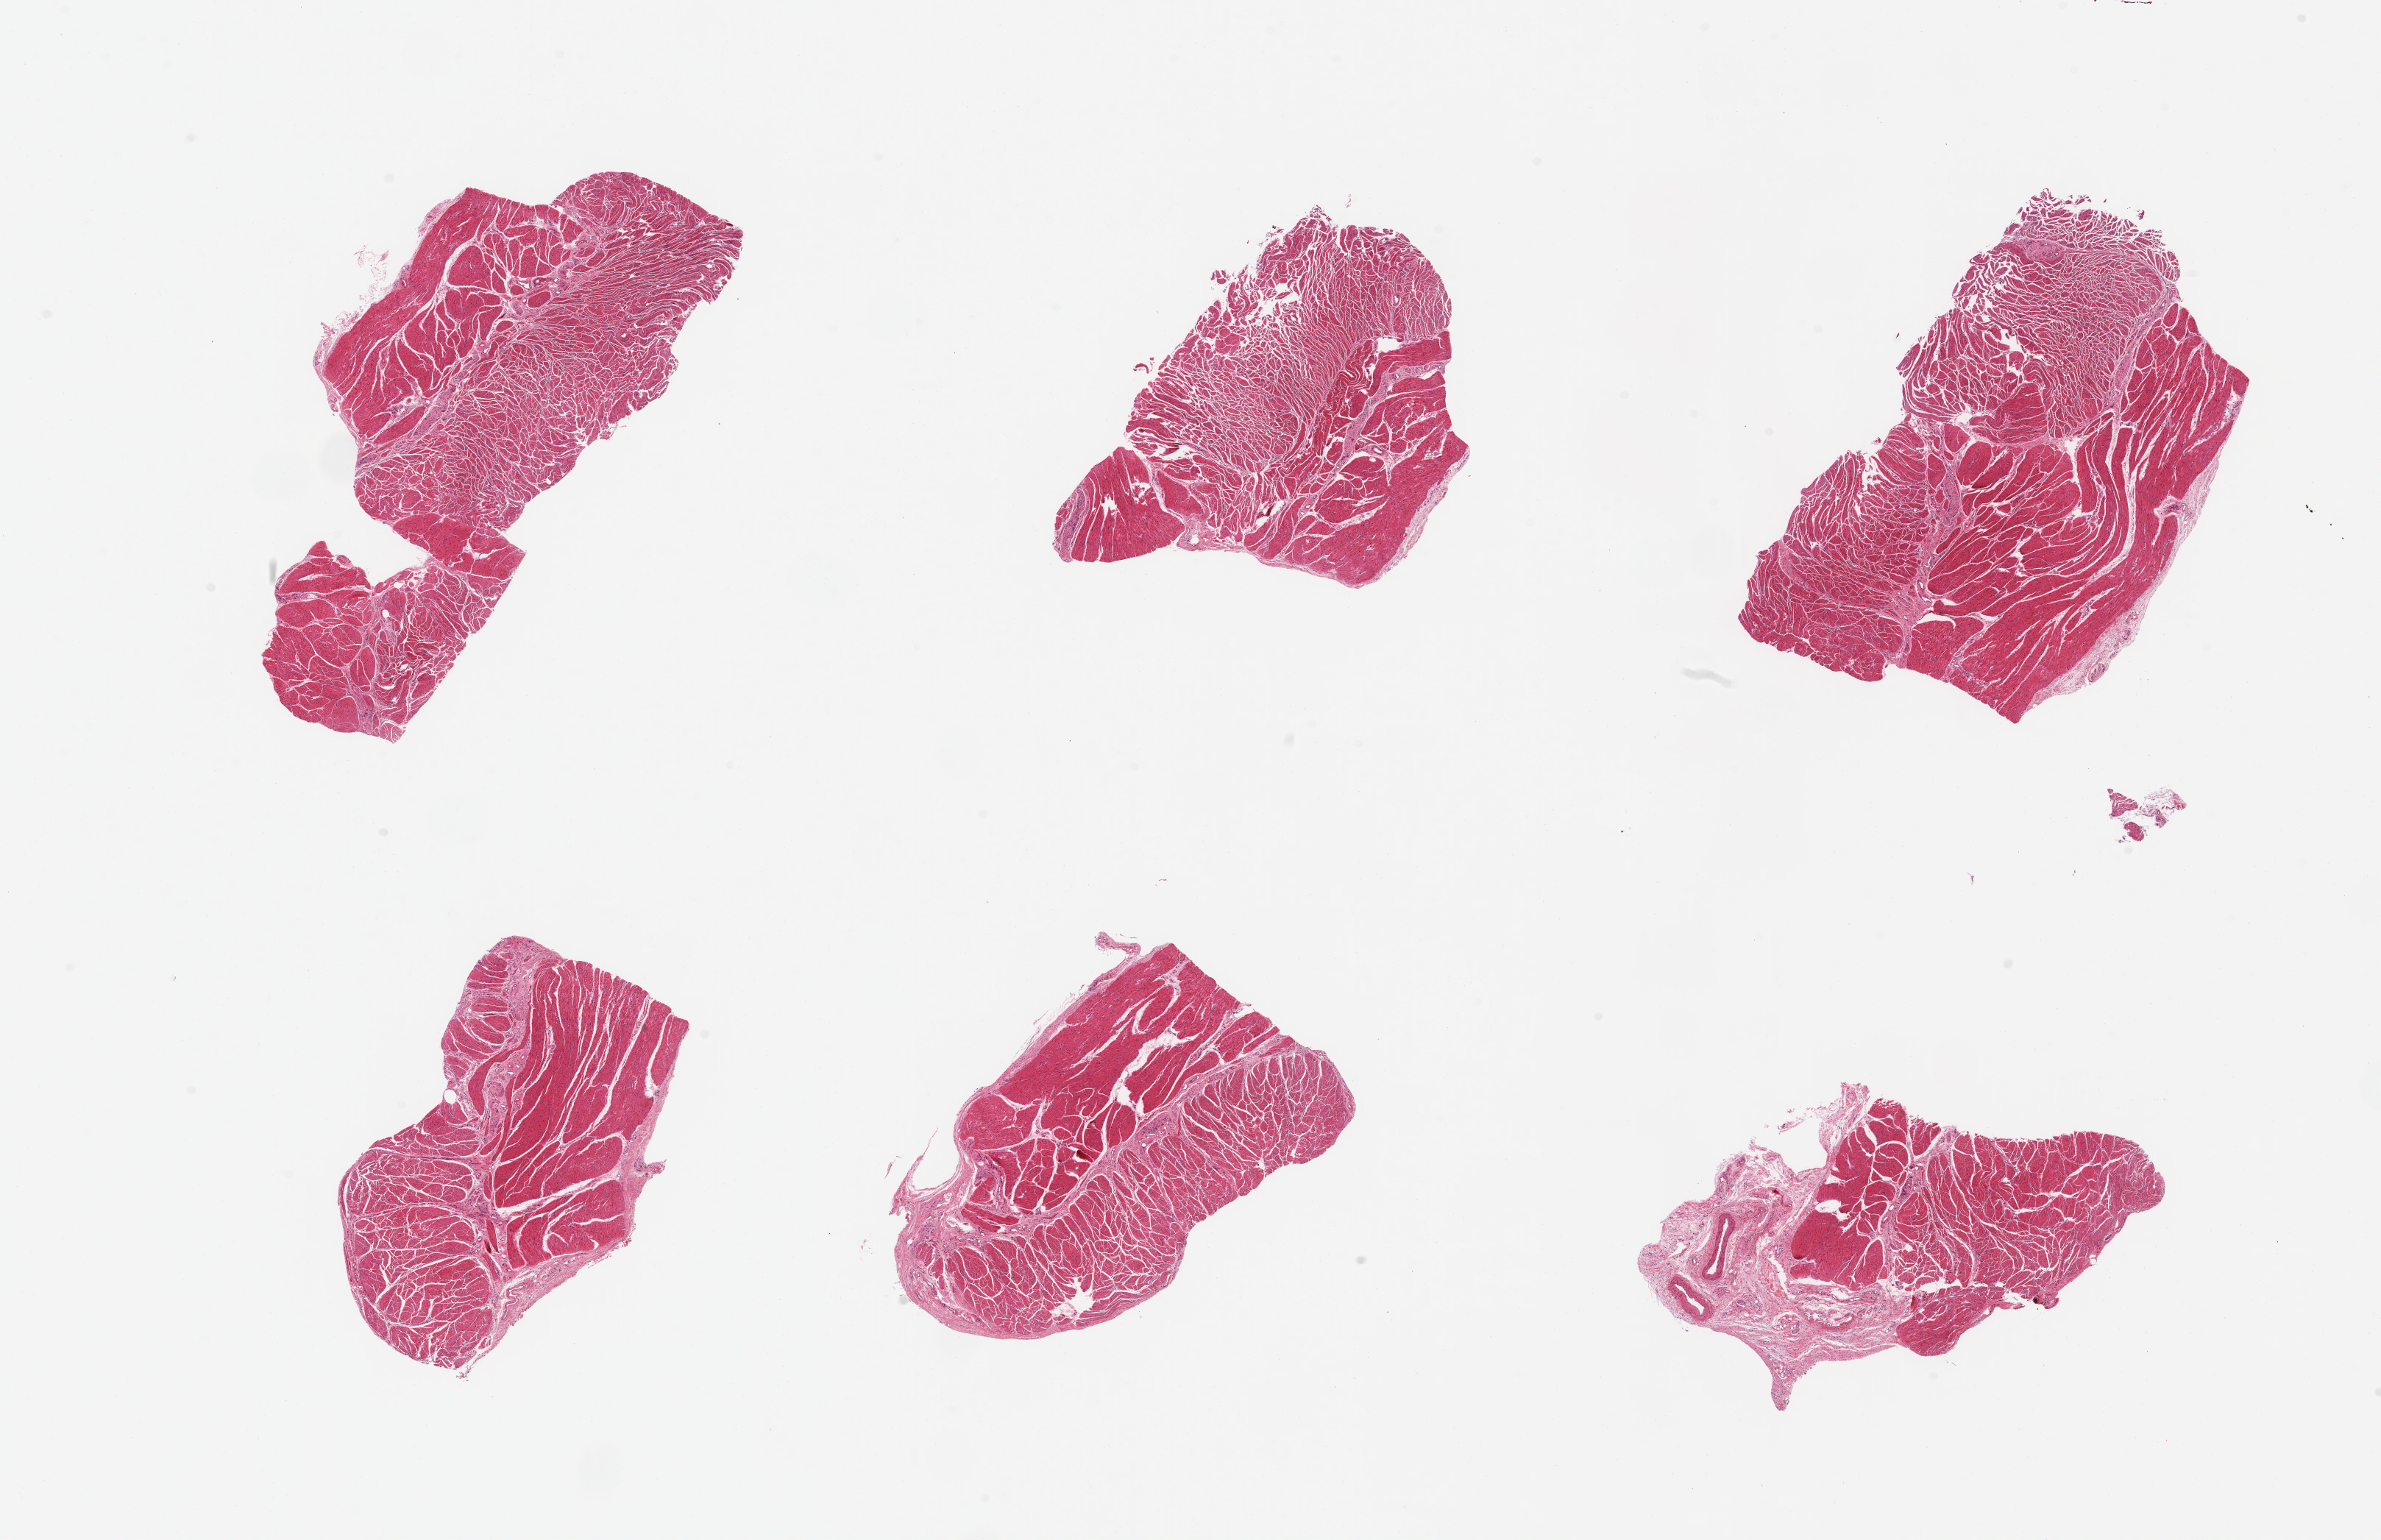
Digitized H&E-stained section, shown as a low-resolution overview of the whole scanned area (about 25.6 x 16.6 mm, acquisition: 20x scan); PAXgene-fixed paraffin-embedded (PFPE) section; section of esophageal muscle (target tissue); donor tissue sample.
Review note (as recorded): 6 pieces; muscularis propria.